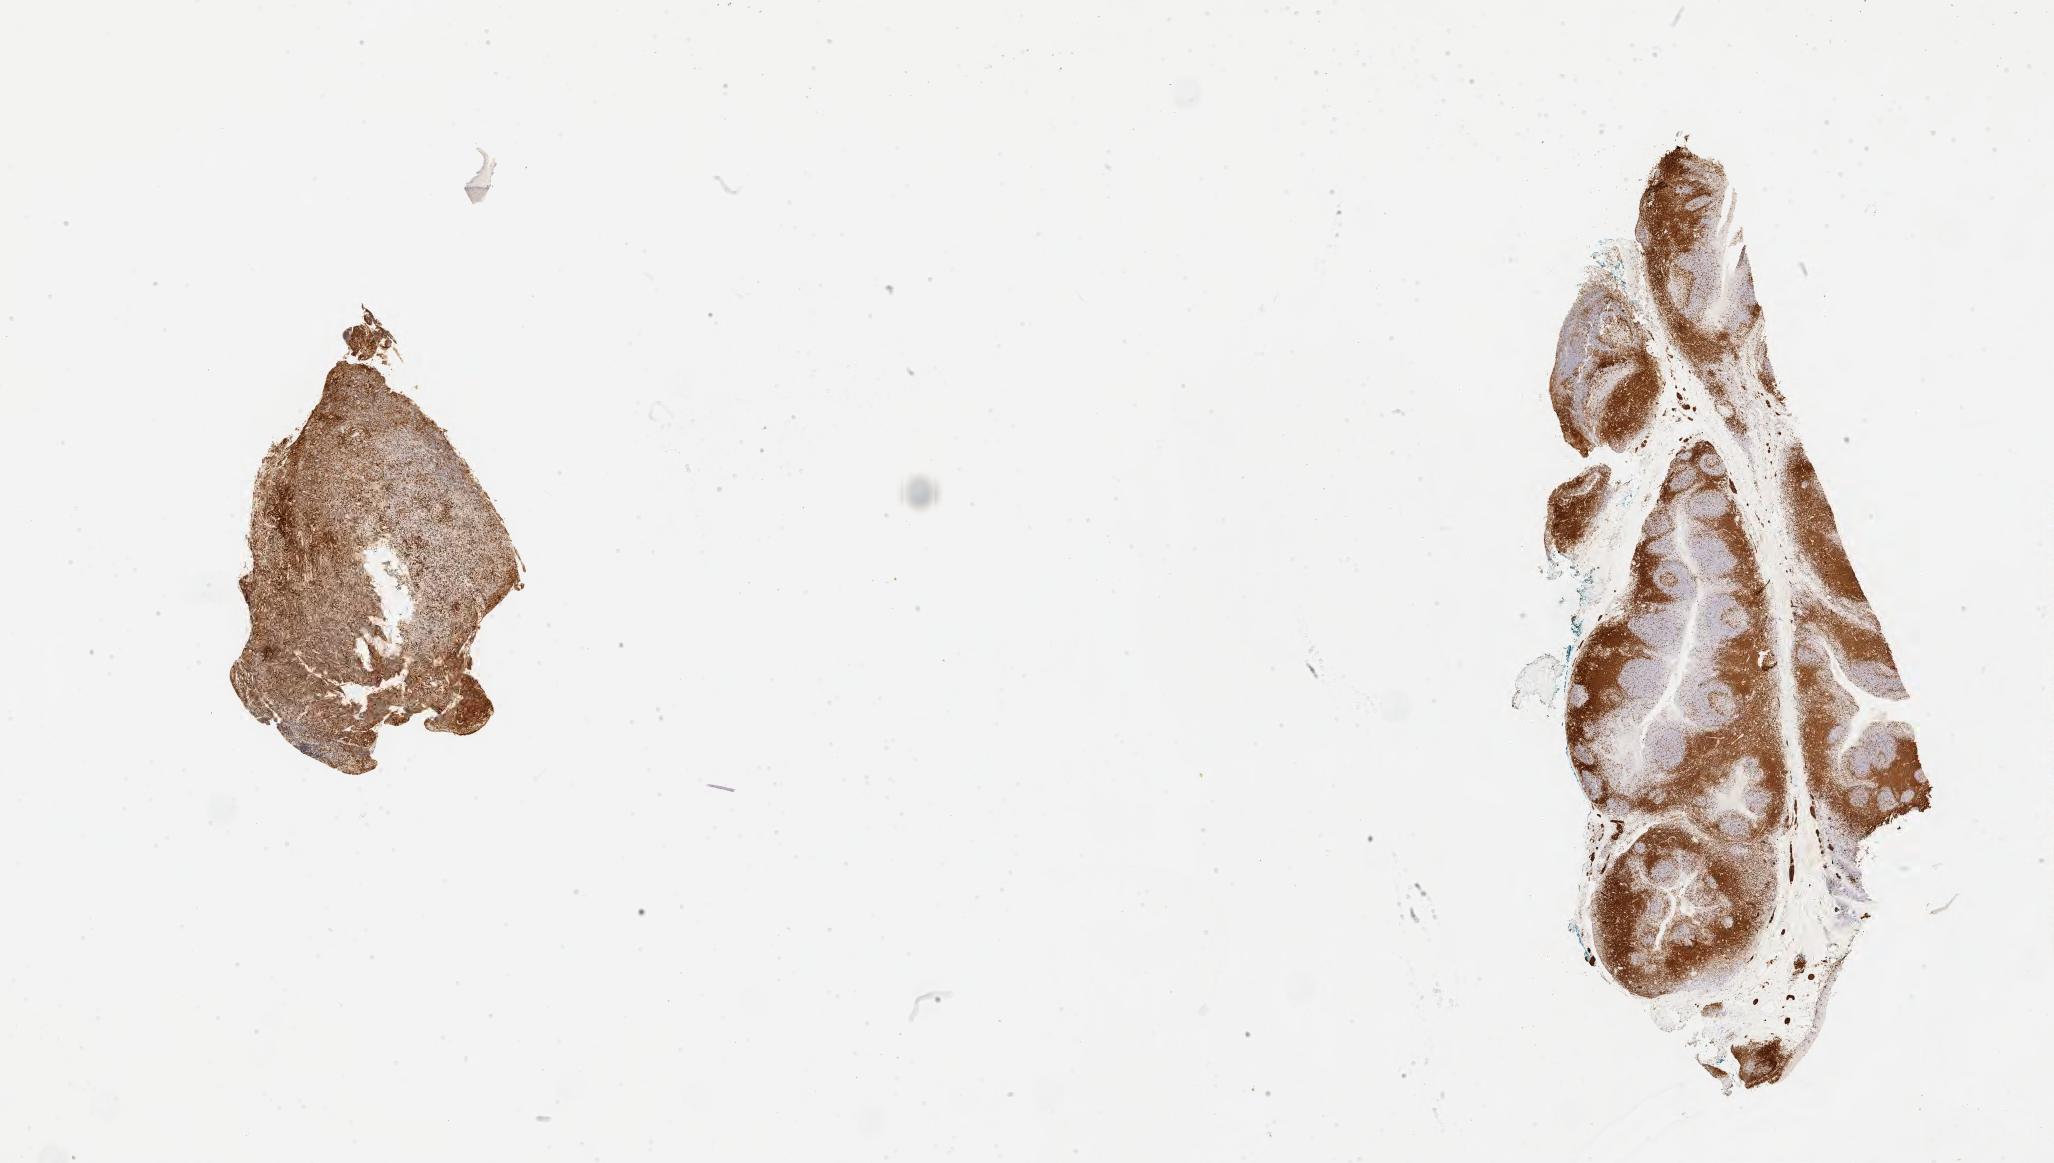
Immunohistochemistry (IHC) whole-slide image stained for CD3, low-resolution overview of the scanned area, about 33.2 x 18.8 mm, specimen: tumor tissue, anatomic site: ovary. Female patient; age at initial diagnosis 3 years.
Histologic diagnosis: Burkitt lymphoma, NOS.